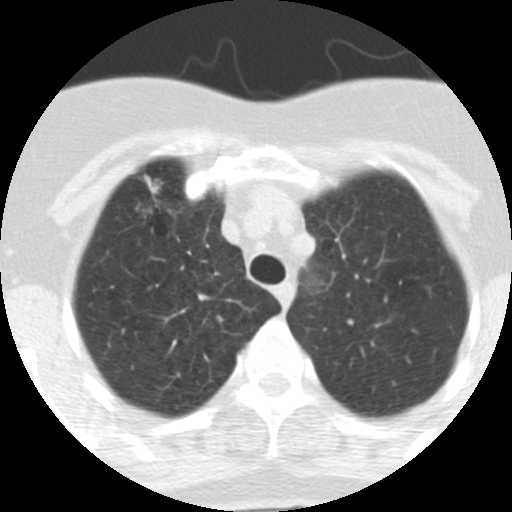
Low-dose screening chest CT, one axial slice; slice 254 of 313 in the series (ordered by position); reconstruction kernel STANDARD; 120 kVp; lung window (W 1500 / L -600 HU); 2.5 mm slice thickness; 512 × 512 image matrix, field of view 253 × 253 mm.
Annotated regions visible in this slice (outlined manually by an expert reader):
- lesion 1 (tumor, upper lobe of right lung): bounding box (x1, y1, x2, y2) in pixels: (144, 175, 159, 194)